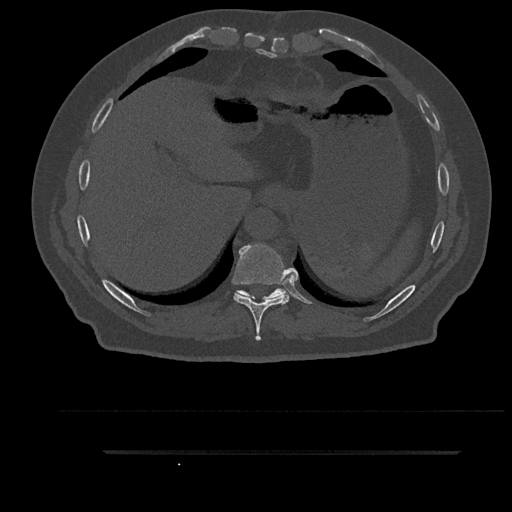
CT including the spine, one axial slice. Position 407 of 797 along the scan axis. 120 kVp. Bone window (W 1800 / L 400 HU). 0.5 mm slice thickness. 512 × 512 image matrix, field of view 432 × 432 mm. Patient: male, 63 years. From the clinical record (not read from this slice): primary cancer: renal; vertebrae with lytic lesions (as recorded): T8.
Annotated regions visible in this slice (semi-automatically segmented with operator editing):
- T10 vertebra: bounding box [x1, y1, x2, y2] px = [234, 288, 286, 300]
- T9 vertebra: [233, 244, 289, 341]